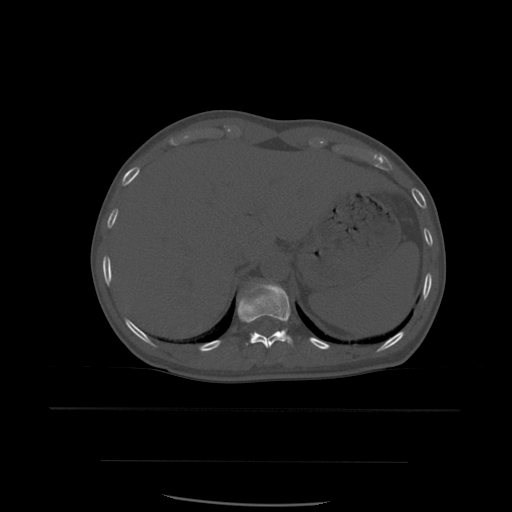
CT including the spine, one axial slice. Position 293 of 574 along the scan axis. Bone window (W 1800 / L 400 HU). 1.25 mm slice thickness. 512 × 512 image matrix, field of view 392 × 392 mm. Patient age 48 years. Case-level facts recorded for this patient, not image findings: primary cancer: lung.
Structures marked on this image (semi-automatically segmented with operator editing):
- T11 vertebra: bounding box (x1, y1, x2, y2) in pixels: (238, 283, 293, 349)